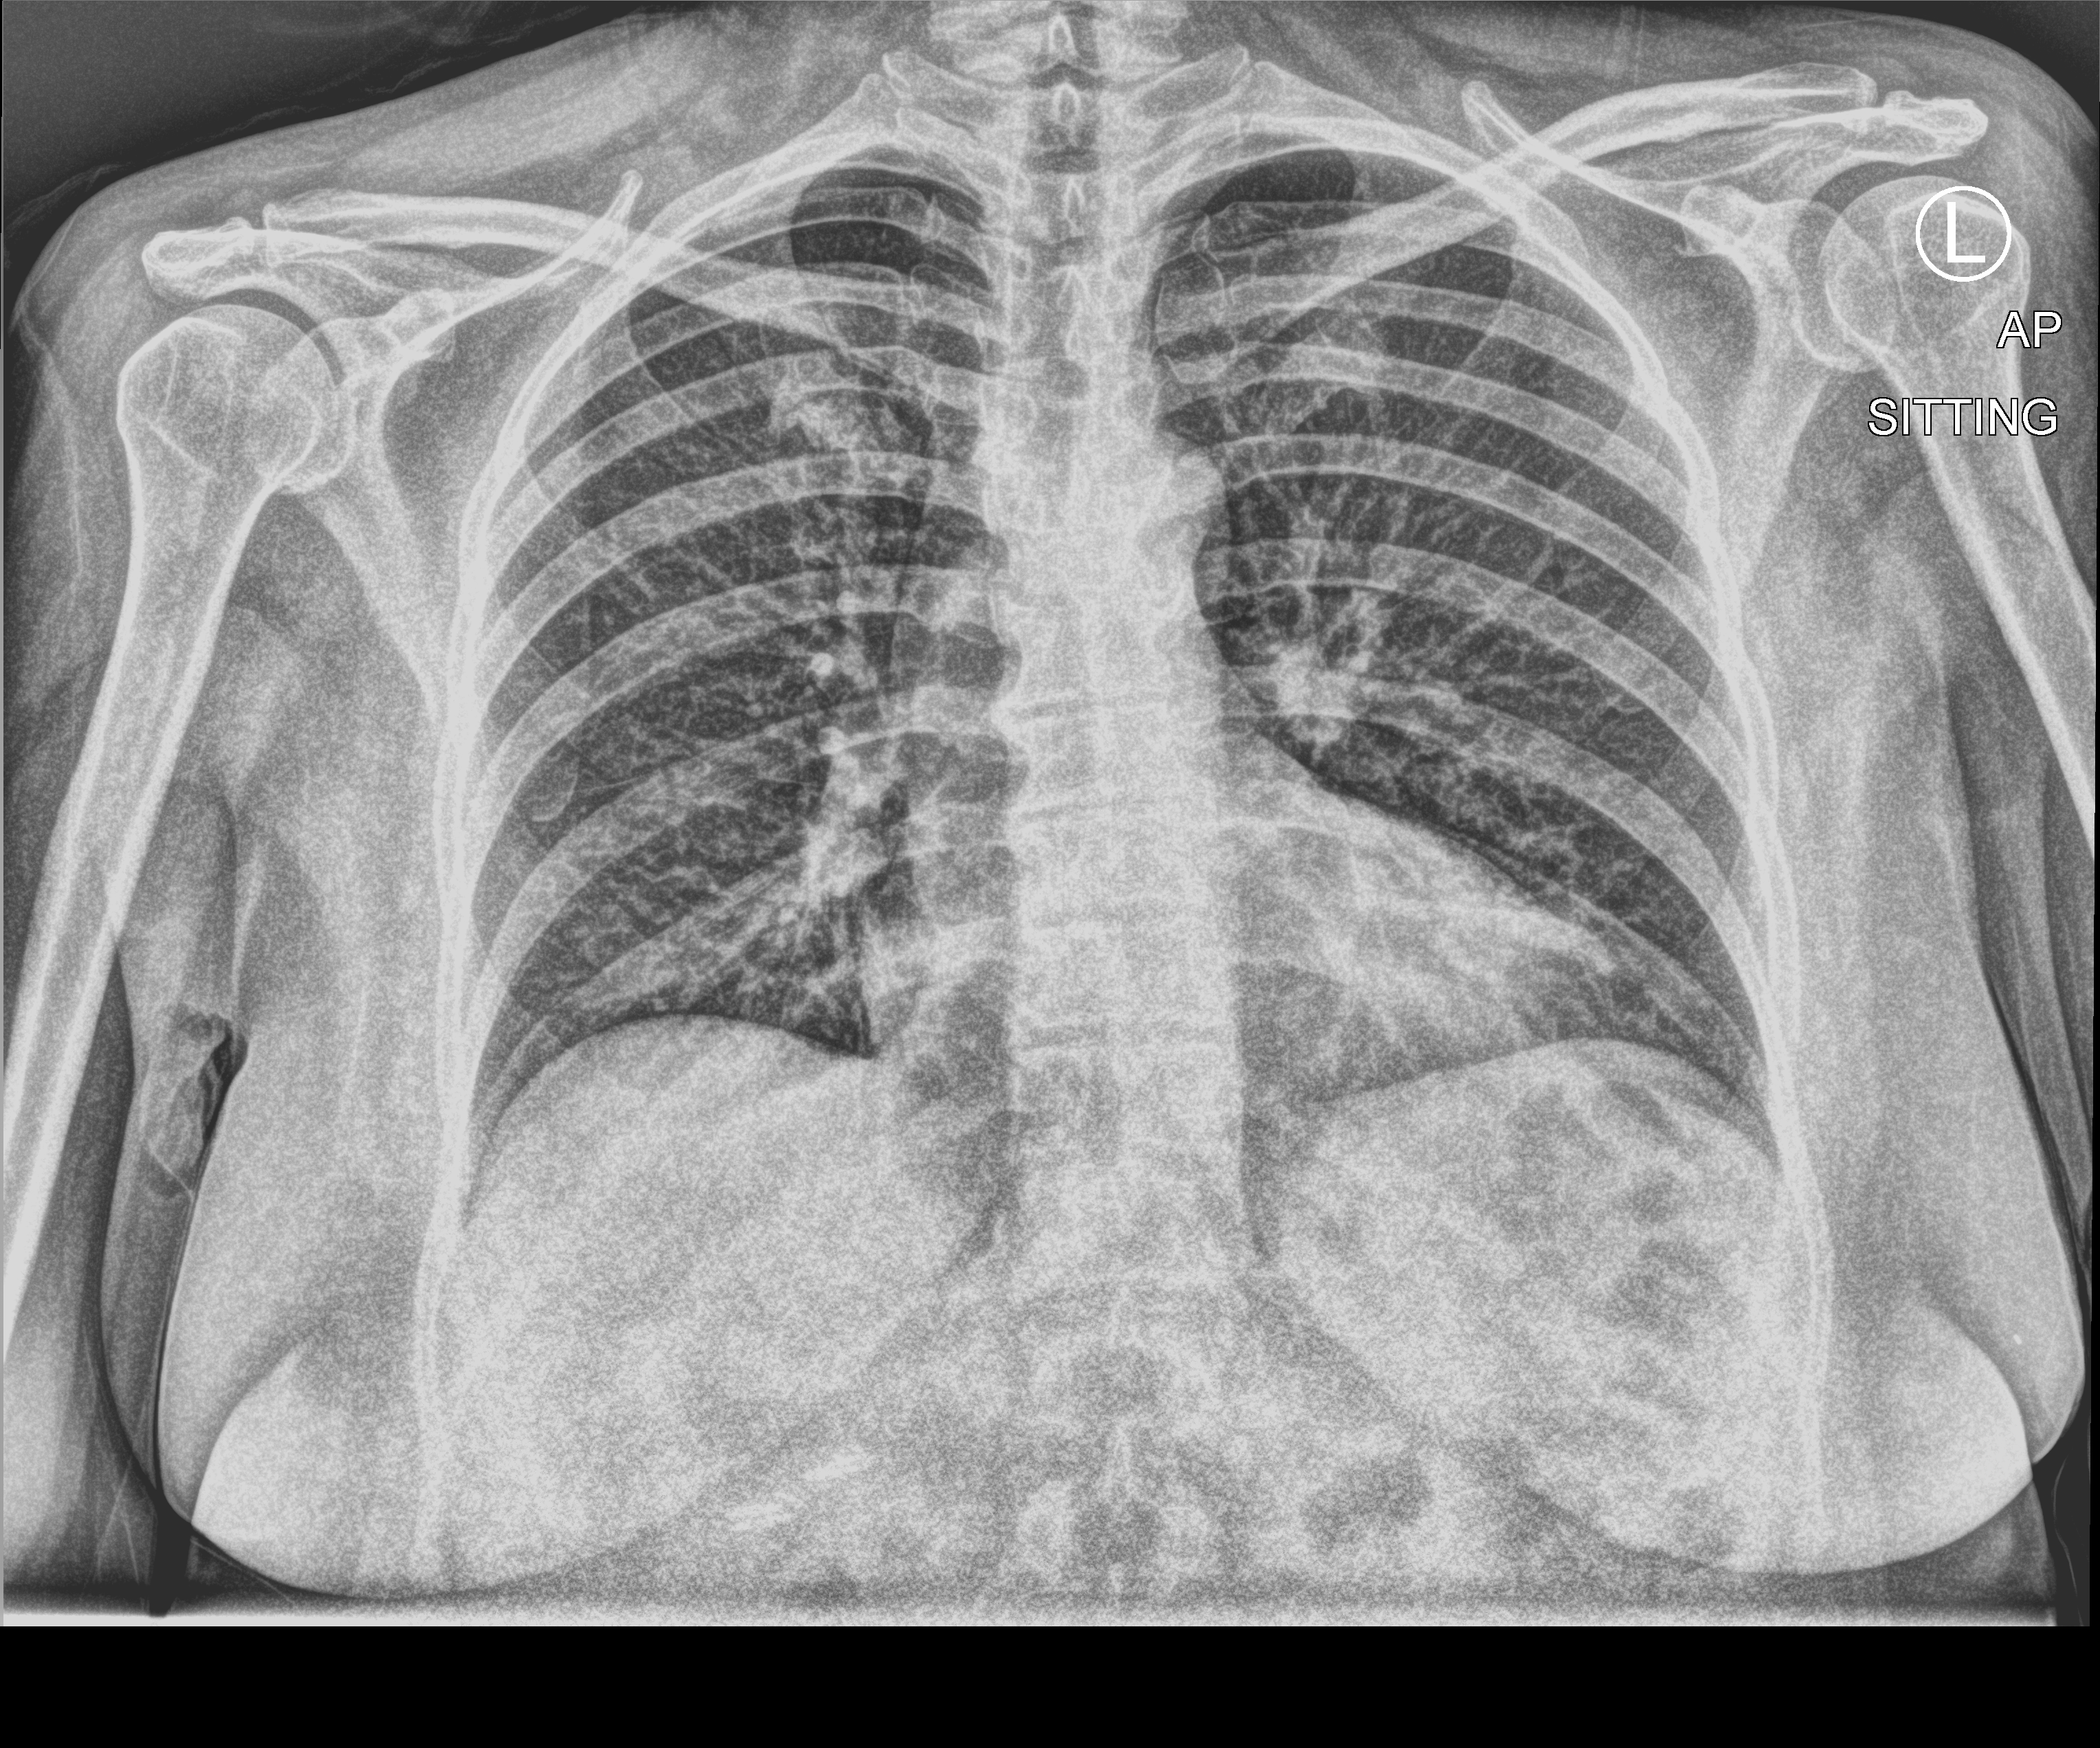
Portable chest radiograph; anteroposterior (AP) projection. Patient hospitalised with COVID-19; female, aged 18–59 years.
From the hospital-stay record, not from the radiograph (when in the stay this image was taken is not recorded): mechanically ventilated during this hospital stay: no.